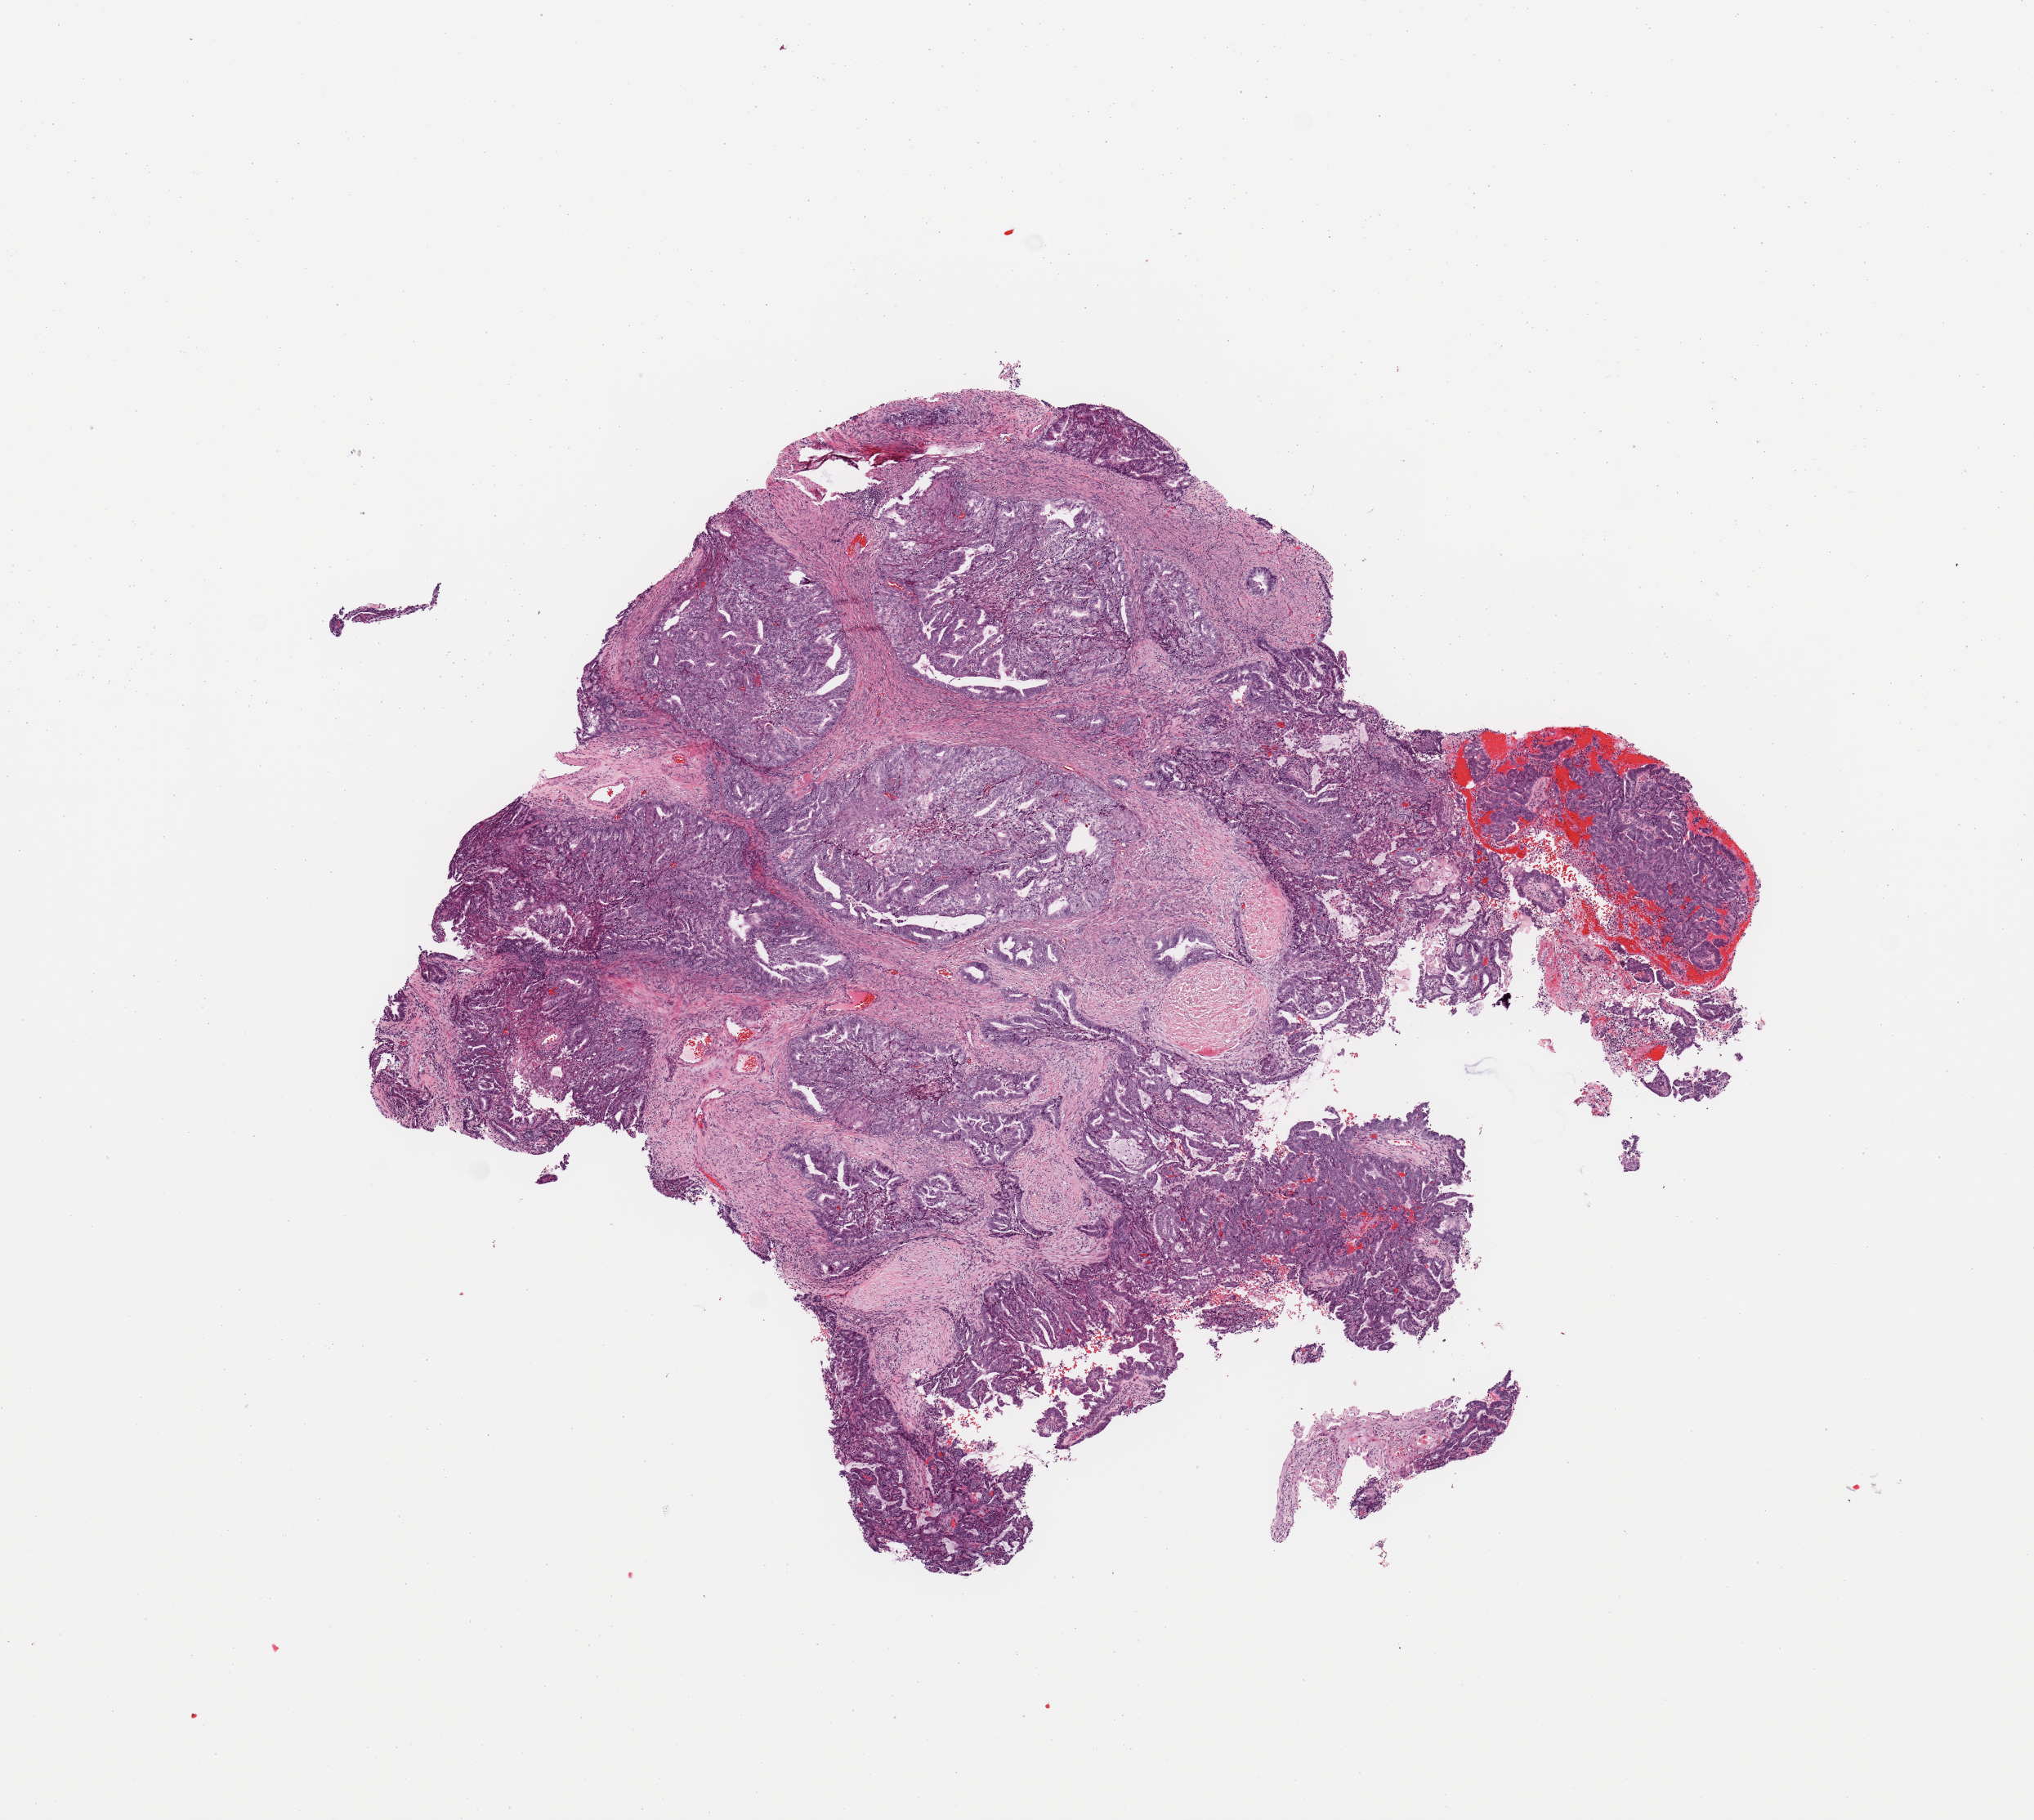
H&E whole-slide image, low-resolution overview of the scanned area, about 9.8 x 8.8 mm (acquisition: 20x scan). Tumour tissue sample, uterus. Female, 59 y/o. Histologic grade: G1 (well differentiated).
* histologic diagnosis: Endometrioid adenocarcinoma, NOS
* AJCC pathologic stage: I